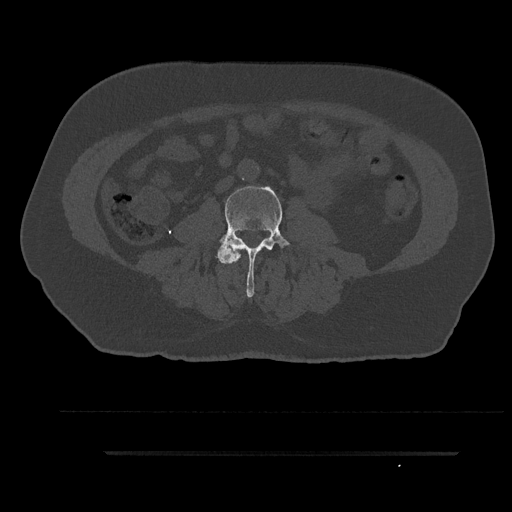
CT including the spine, one axial slice. Slice 38 of 797 in the series (ordered by position). 120 kVp. Bone window (W 1800 / L 400 HU). 0.5 mm slice thickness. 512 × 512 image matrix, field of view 432 × 432 mm. Patient: male, 63 years. Case-level facts recorded for this patient, not image findings: primary cancer: renal.
Outlined on this slice (semi-automatic segmentation, software-assisted and operator-edited):
- L3 vertebra: box from (x=215, y=185) to (x=291, y=298) px